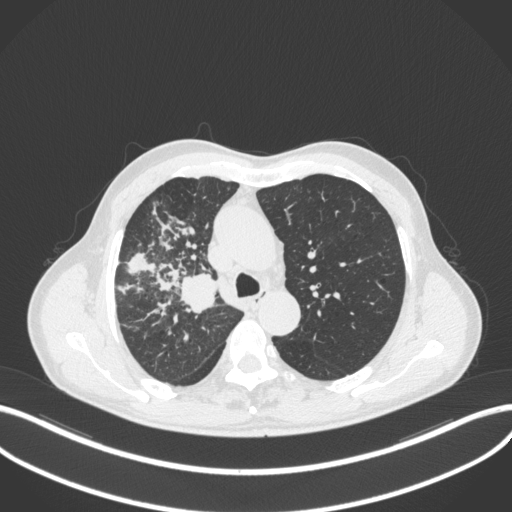
Chest CT, one axial slice. Slice 339 of 490 in the series (ordered by position). 120 kVp. Lung window (W 1500 / L -600 HU). 1 mm slice thickness. 512 × 512 image matrix. Male patient, age 69 years. From the clinical record (not read from this slice): clinical TNM (as recorded): T2a N0 M0.
Annotated regions visible in this slice (rectangle marked by the reading radiologist):
- lung tumour (recorded histology: adenocarcinoma): box from (x=176, y=272) to (x=221, y=318) px